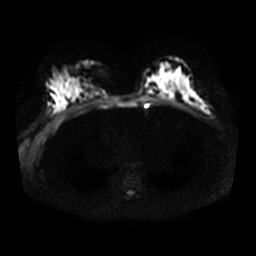
Breast MRI, one axial slice. Slice 18 of 32 in the series (ordered by position). Diffusion-weighted series; image 2 of 4 stored at this slice position (different b-values; order by instance number). 3 T. 5 mm slice thickness. 256 × 256 image matrix, field of view 340 × 340 mm. Female patient.
Structures marked on this image (manually delineated by an expert):
- tumour on diffusion-weighted imaging: bounding box [x1, y1, x2, y2] px = [200, 104, 208, 114]